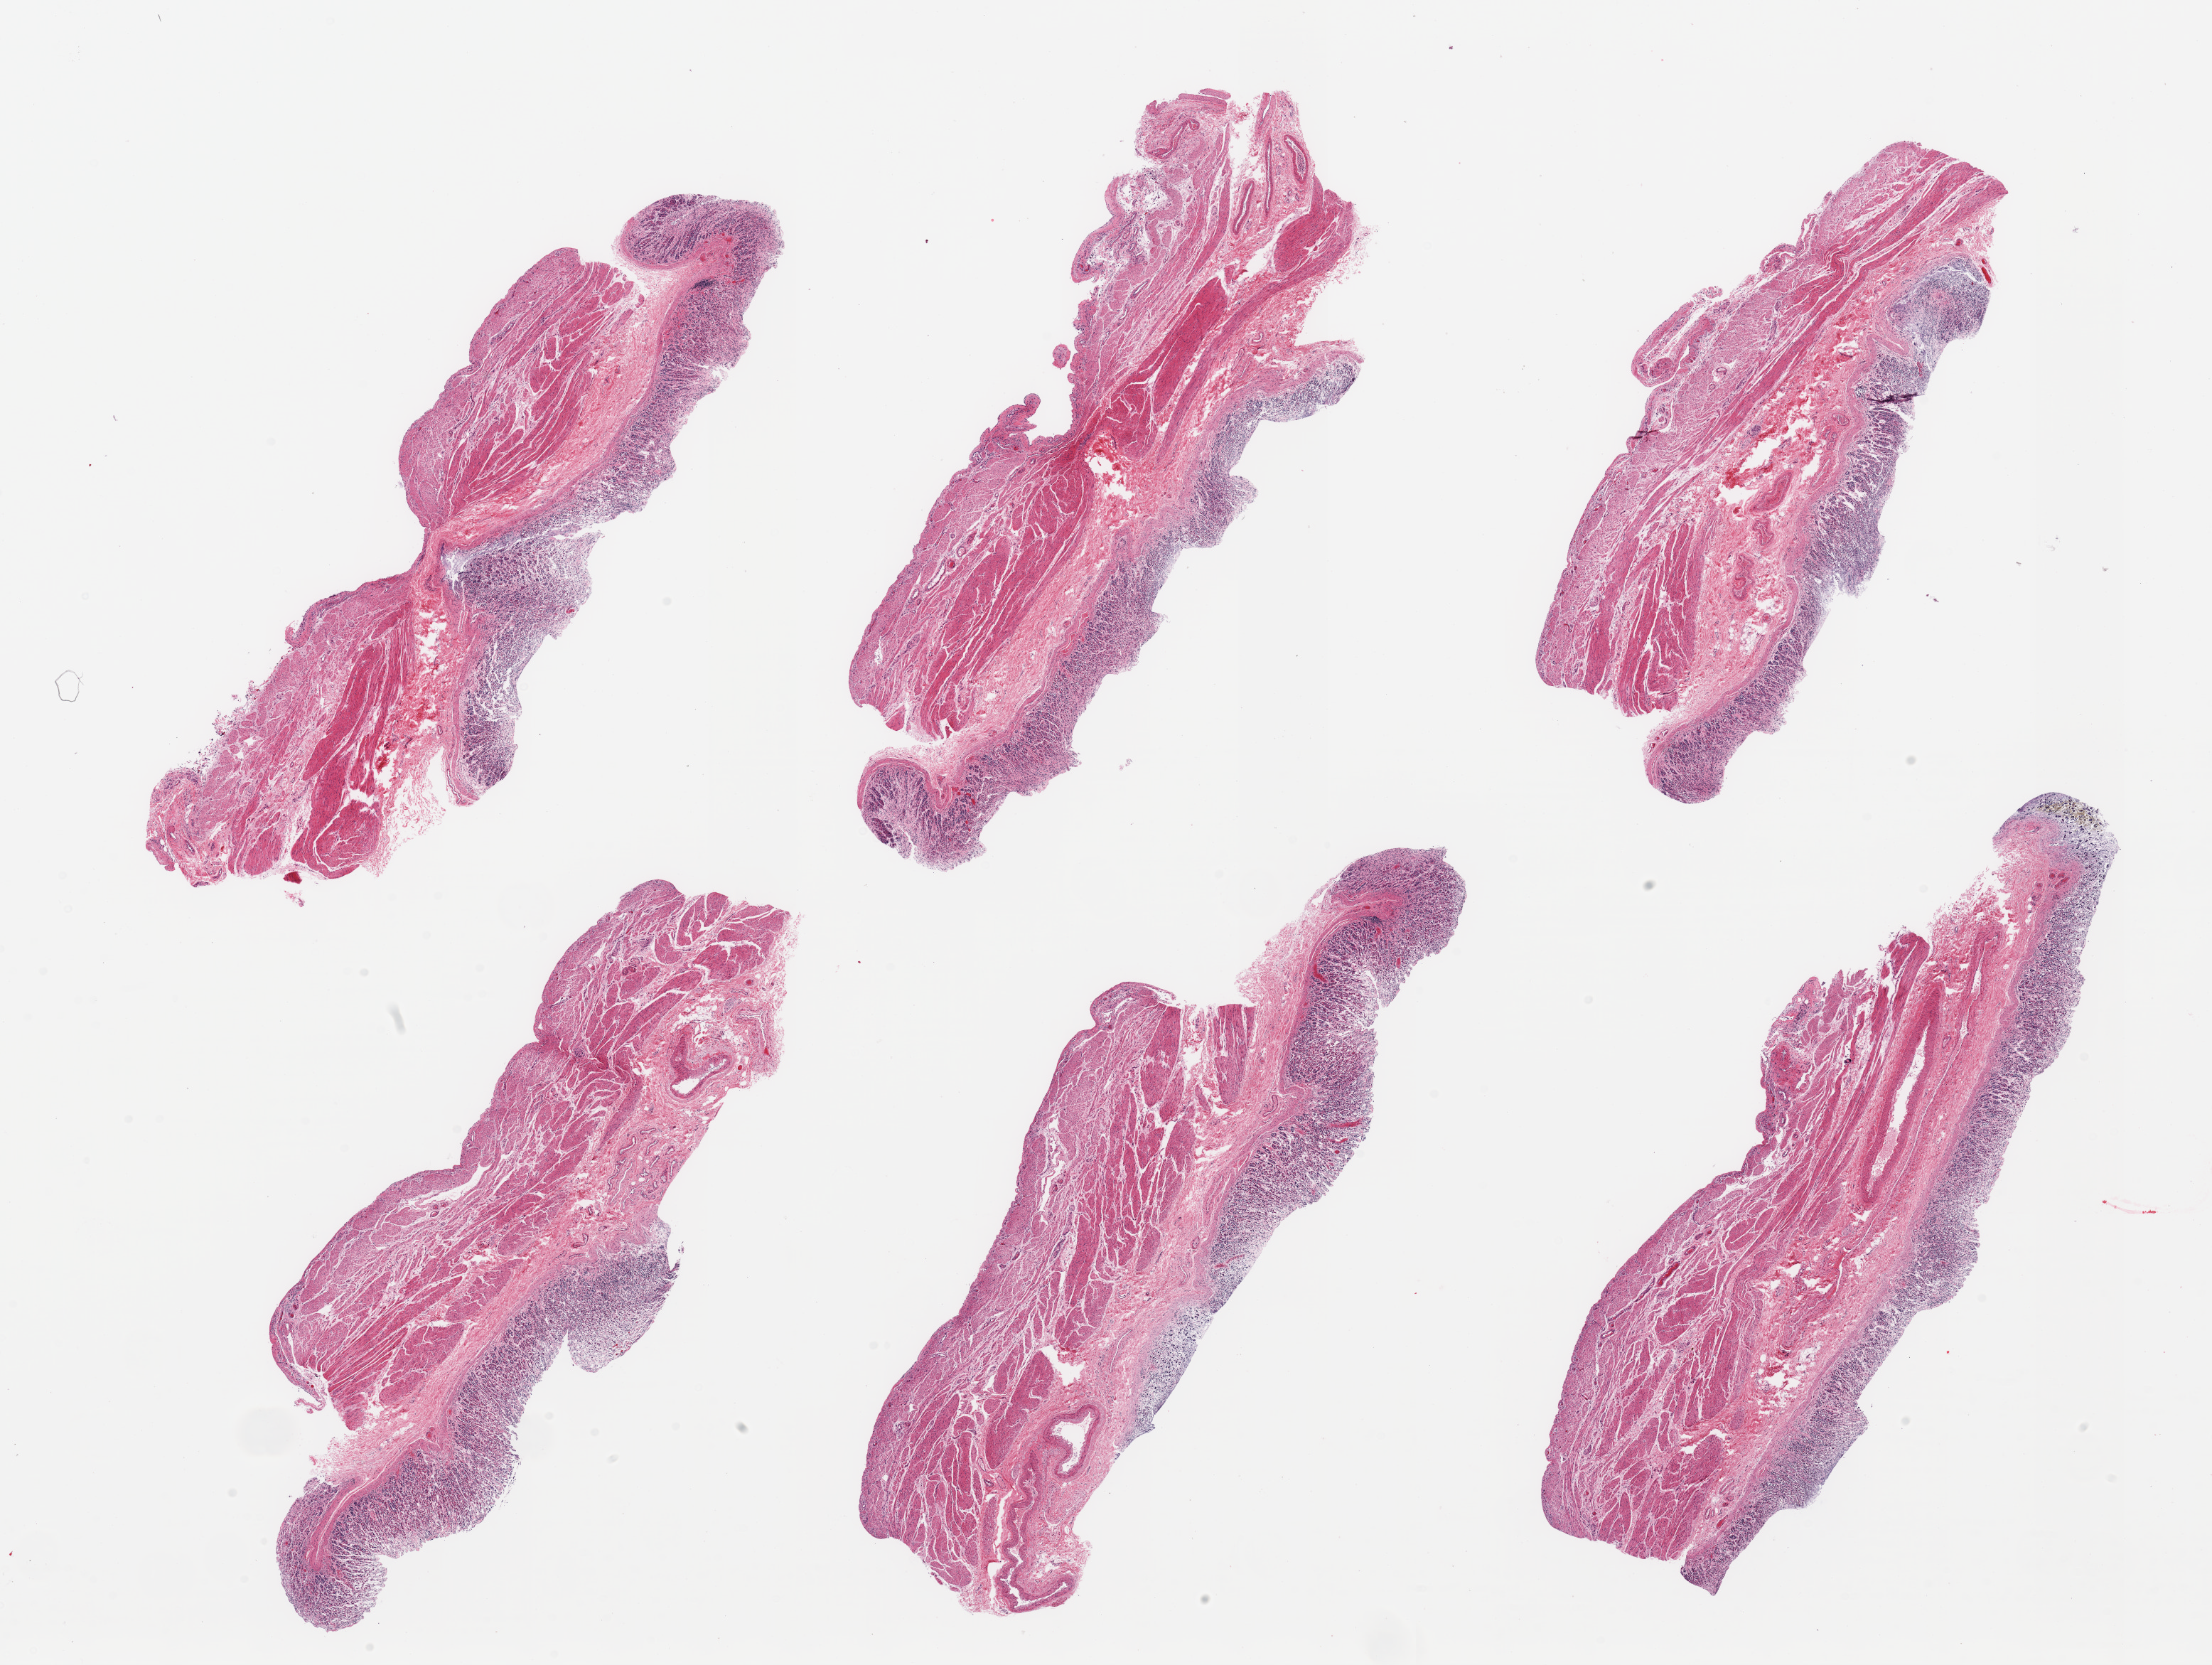
Whole-slide image, H&E stain — a low-resolution overview of the entire scanned area, about 24.6 x 18.5 mm (from a 20x scan). PAXgene-fixed, paraffin-embedded tissue. Section of stomach (target tissue). Tissue donor sample. Donor sex: male.
Pathologist's review note for this sample: 6 pieces, mucosa up to ~0.7mm, advanced autolysis.